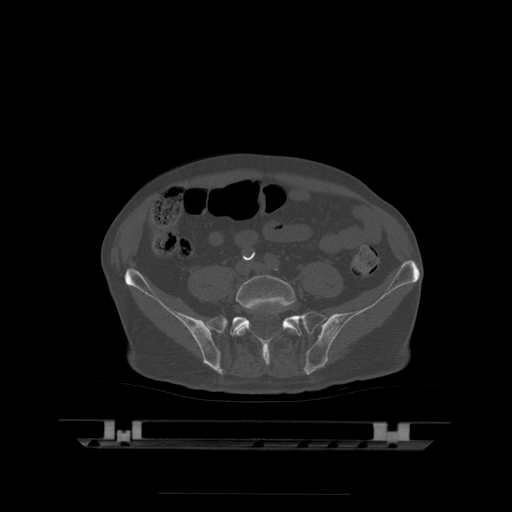
CT including the spine, one axial slice; position 64 of 522 along the scan axis; bone window (W 1800 / L 400 HU); 1.25 mm slice thickness; 512 × 512 image matrix, field of view 436 × 436 mm. Patient age 68 years. From the clinical record (not read from this slice): primary cancer: urothelial.
Structures marked on this image (semi-automatic segmentation, software-assisted and operator-edited):
- L5 vertebra: box from (x=236, y=275) to (x=295, y=336) px